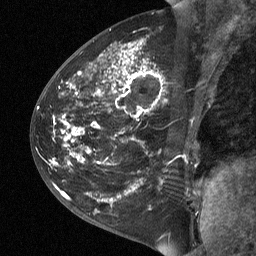
Breast MRI (dynamic contrast-enhanced), one sagittal slice; position 27 of 64 along the scan axis; dynamic contrast-enhanced study with each time point stored as its own series, time point 2 of 3 at this slice position (early post-contrast, ordered by acquisition time); 1.5 T; TE 4.8 ms, TR 27 ms; 2 mm slice thickness; 256 × 256 image matrix. Patient: female, 42 years. Case-level facts recorded for this patient, not image findings: setting: breast cancer imaged before/during neoadjuvant chemotherapy; receptor status: triple-negative.
Structures marked on this image (semi-automatically segmented with operator editing):
- analysis volume of interest (the breast-tissue region the enhancement analysis was run in; not a lesion): bounding box (x1, y1, x2, y2) in pixels: (43, 29, 203, 190)
- tumour enhancement mask (voxels above the 90 % enhancement threshold inside the analysis volume of interest): (73, 44, 149, 160)